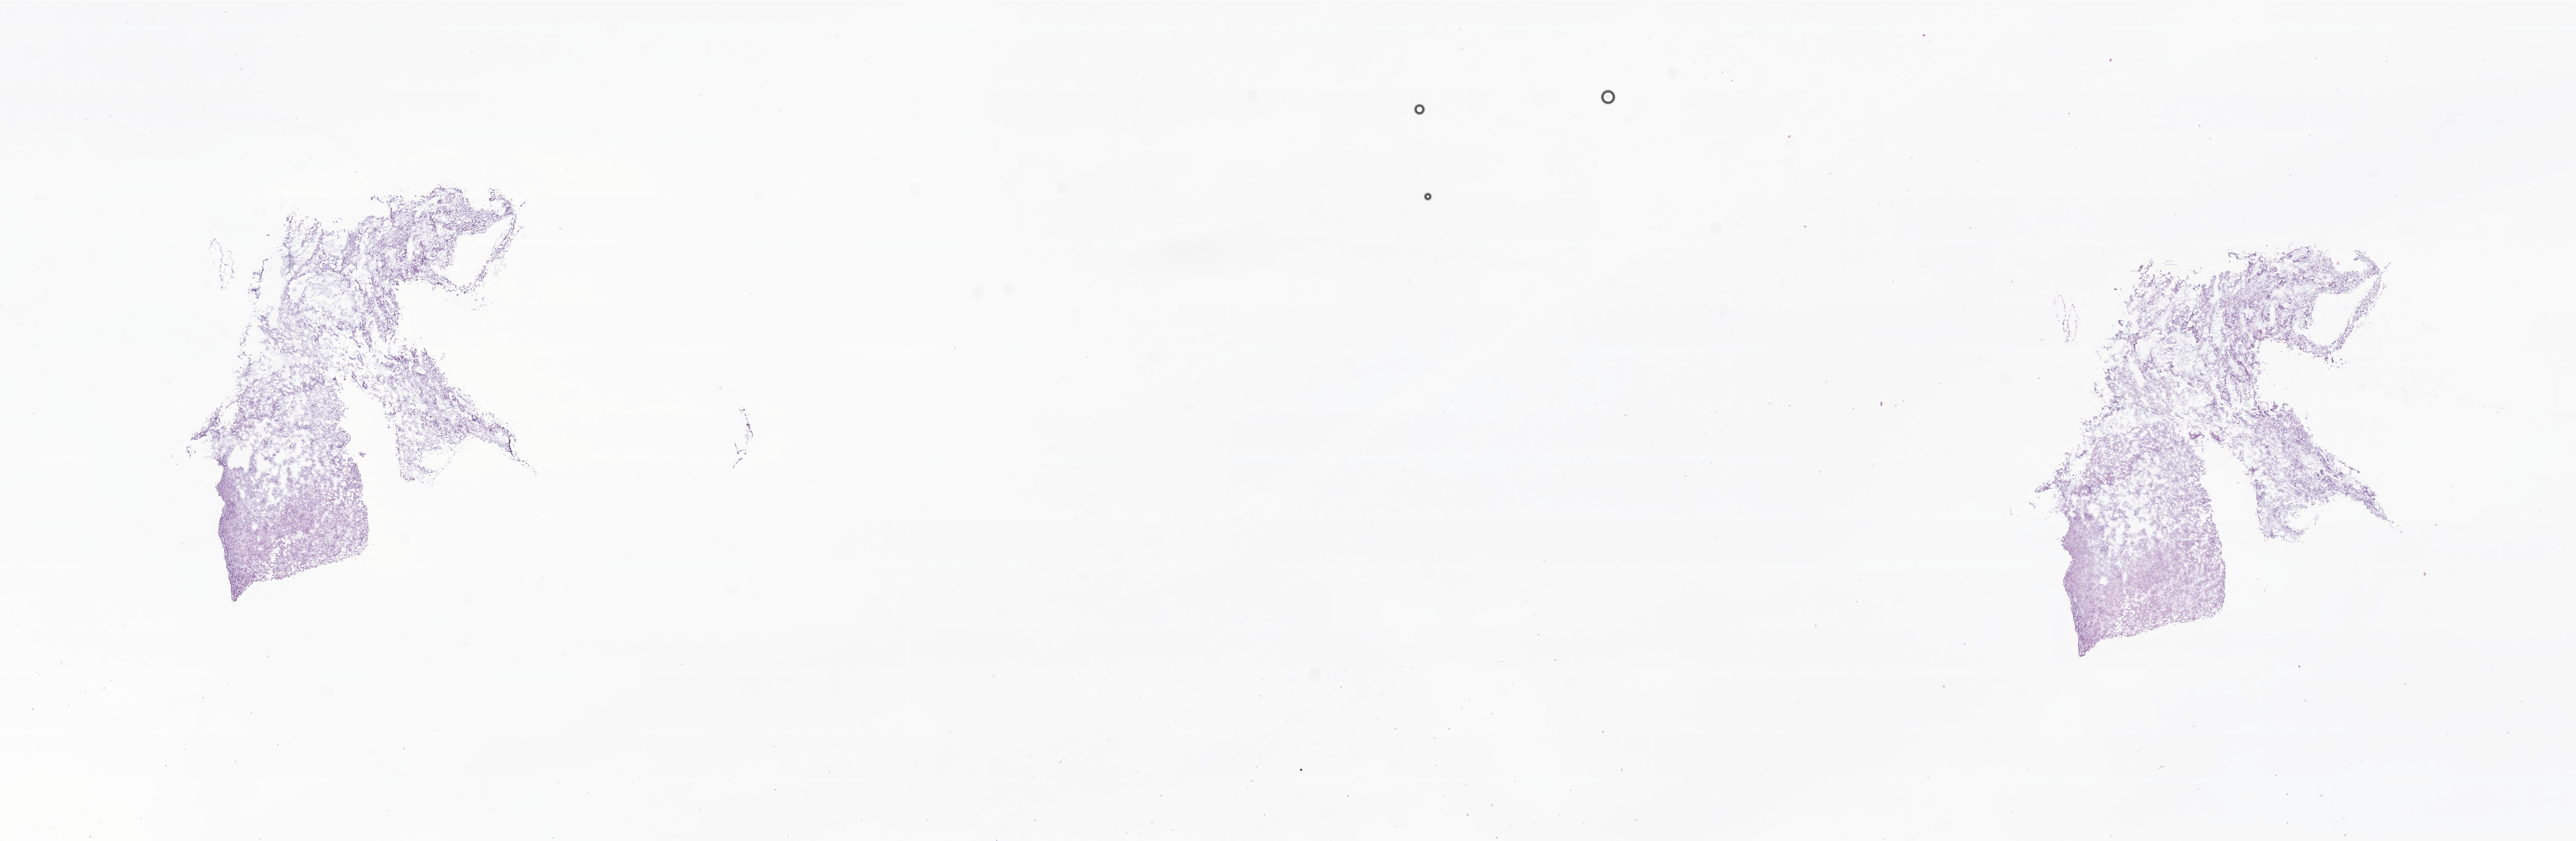
Whole-slide image, haematoxylin and eosin stain of tumor tissue from the brain, a low-resolution overview of the entire scanned area, about 25.6 x 8.4 mm; cryosection (OCT / tissue freezing medium). Patient male; age 249 months (20 years 9 months).
Diagnosis (ICD-O-3 morphology term): Pilocytic astrocytoma.